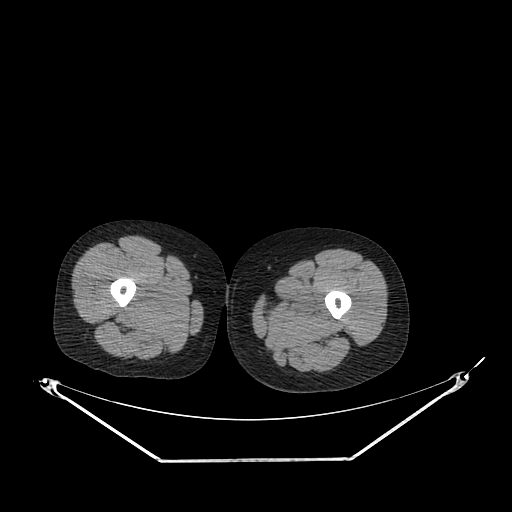
CT of an extremity soft-tissue mass (from a PET/CT study), one axial slice. Position 221 of 267 along the scan axis. Soft-tissue window (W 400 / L 40 HU). 3.75 mm slice thickness. 512 × 512 image matrix, field of view 500 × 500 mm. Female patient. Case-level facts recorded for this patient, not image findings: histological type: pleiomorphic leiomyosarcoma; grade: intermediate; site of the primary tumour: left thigh.
Structures marked on this image (expert contour drawn on MRI and transferred to this co-registered scan by the dataset authors):
- gross tumour volume including surrounding oedema: box from (x=265, y=294) to (x=325, y=318) px